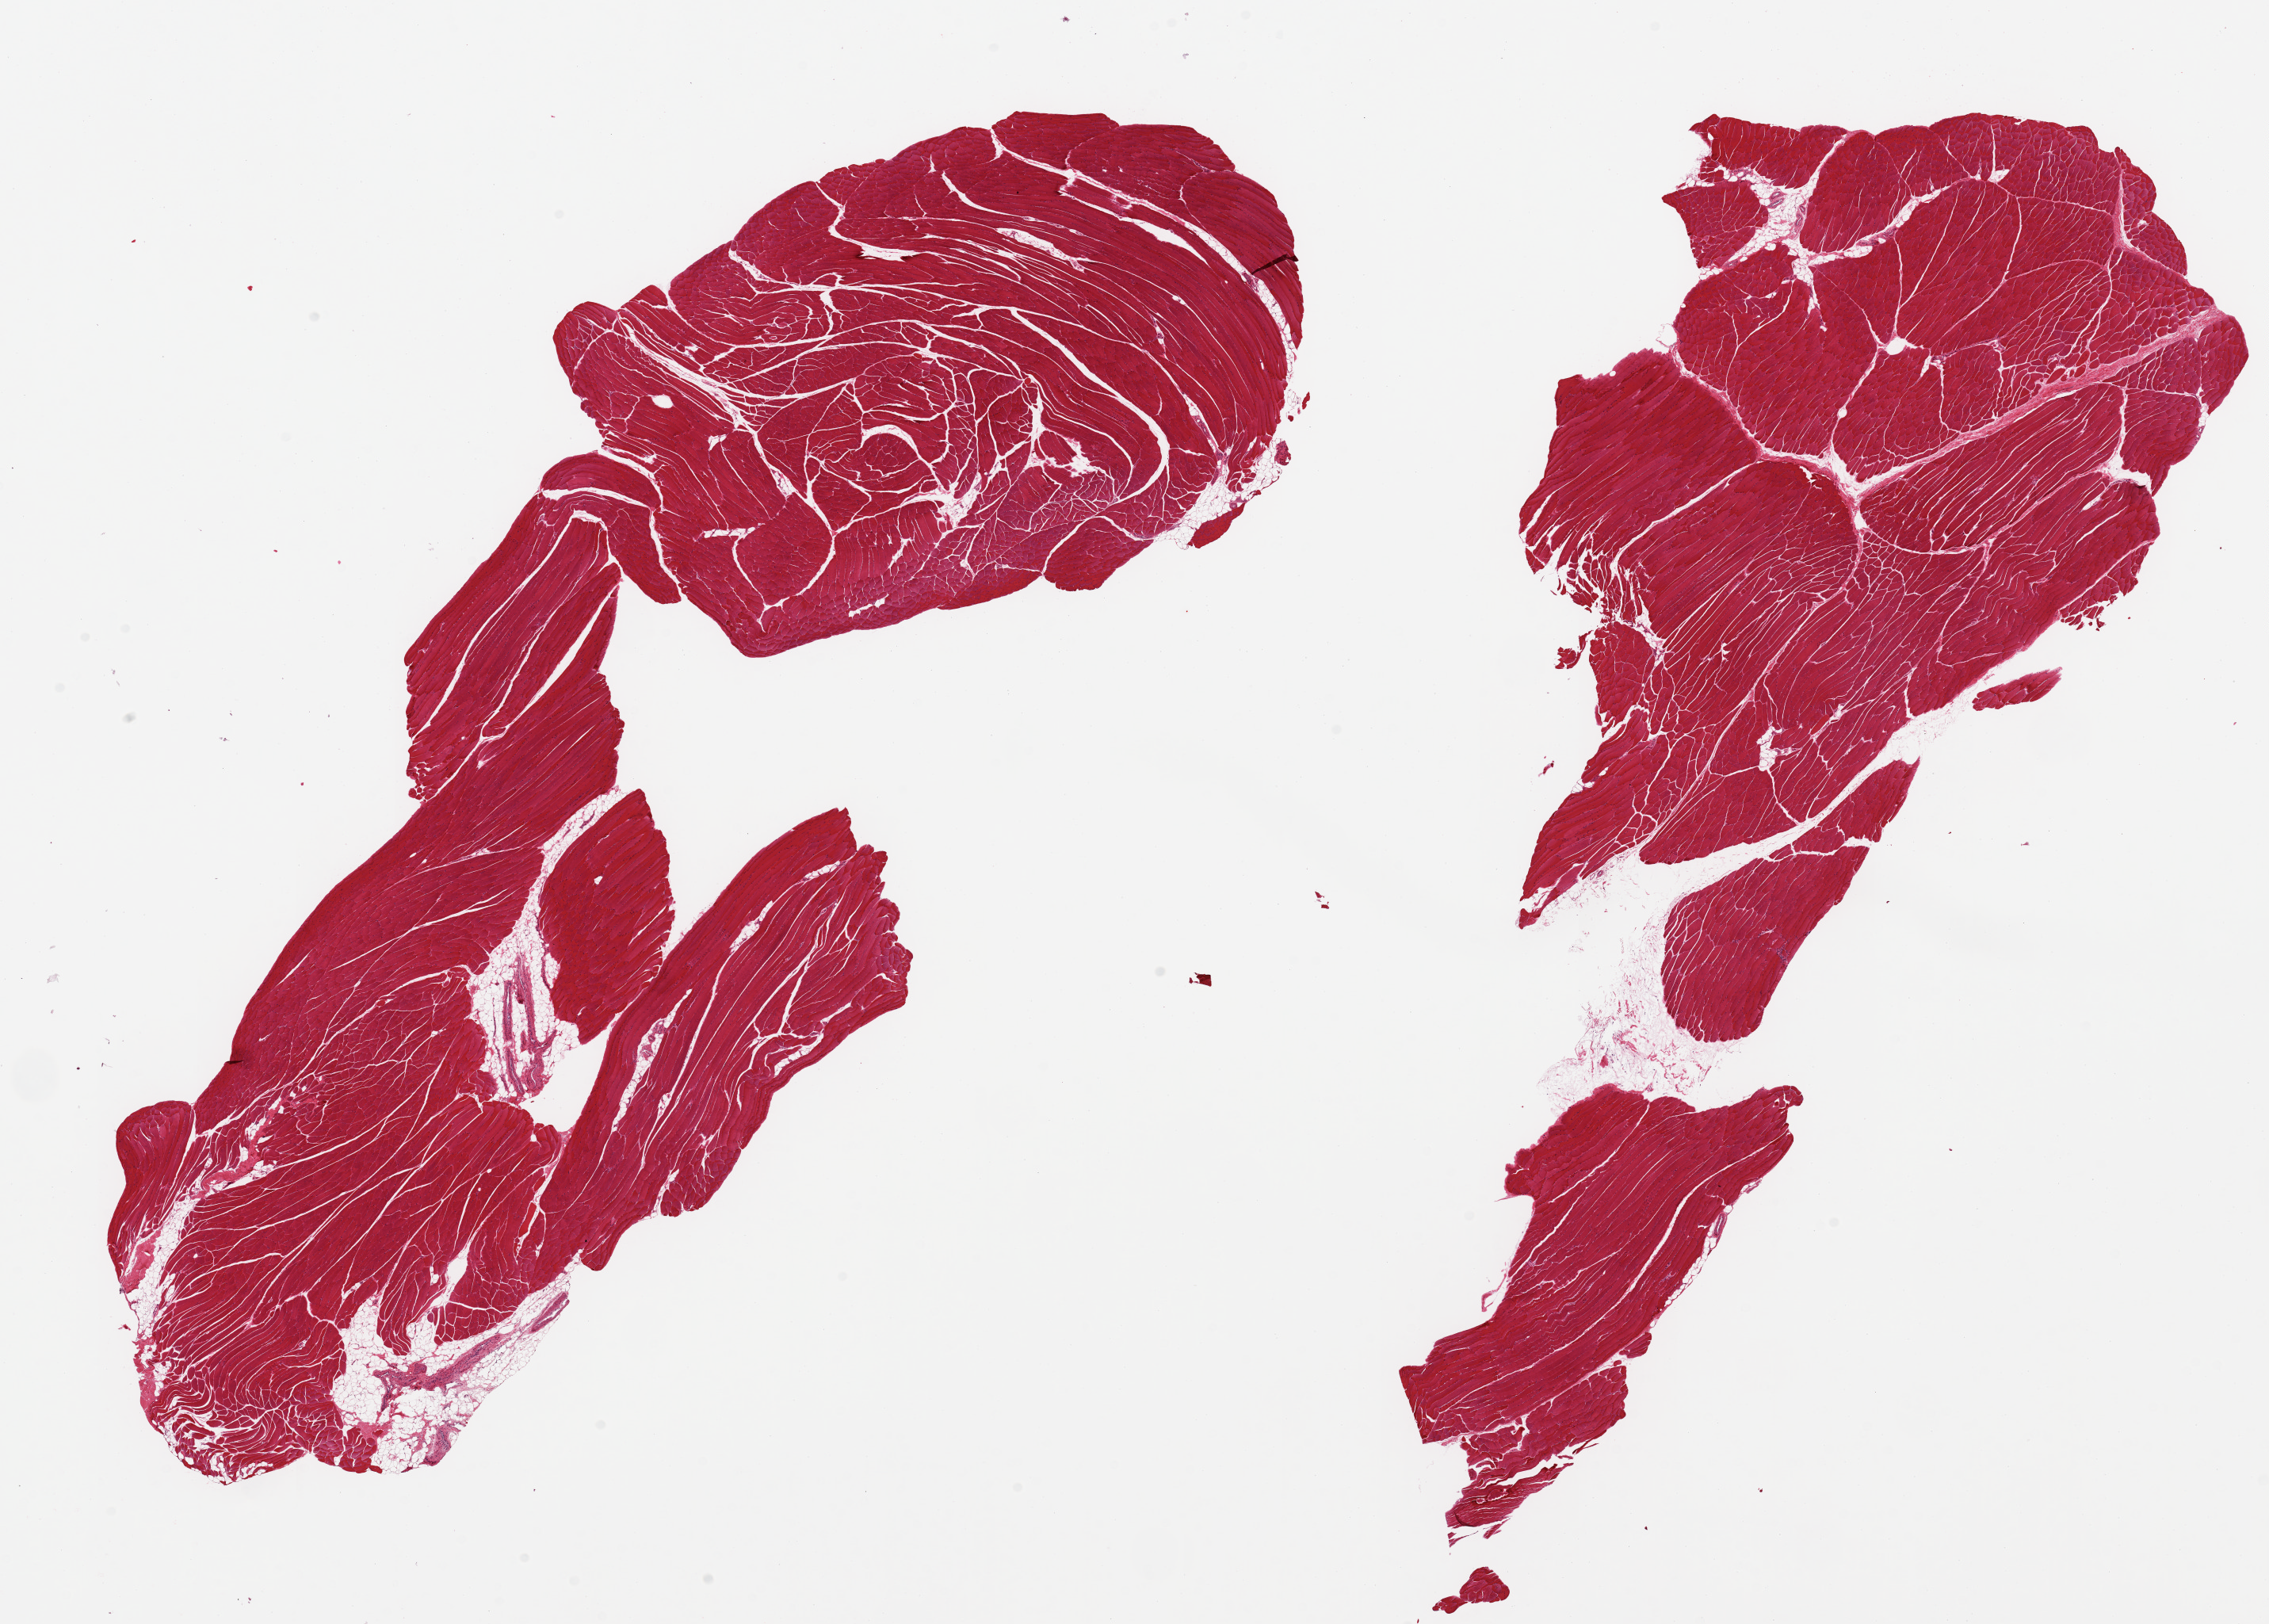
Haematoxylin and eosin whole-slide image, whole scanned area (about 22.6 x 16.2 mm) shown as a low-resolution overview, PAXgene-fixed paraffin-embedded (PFPE) section, section of skeletal muscle (target tissue), tissue donor sample. Donor: female.
- review note (as recorded): 2 pieces